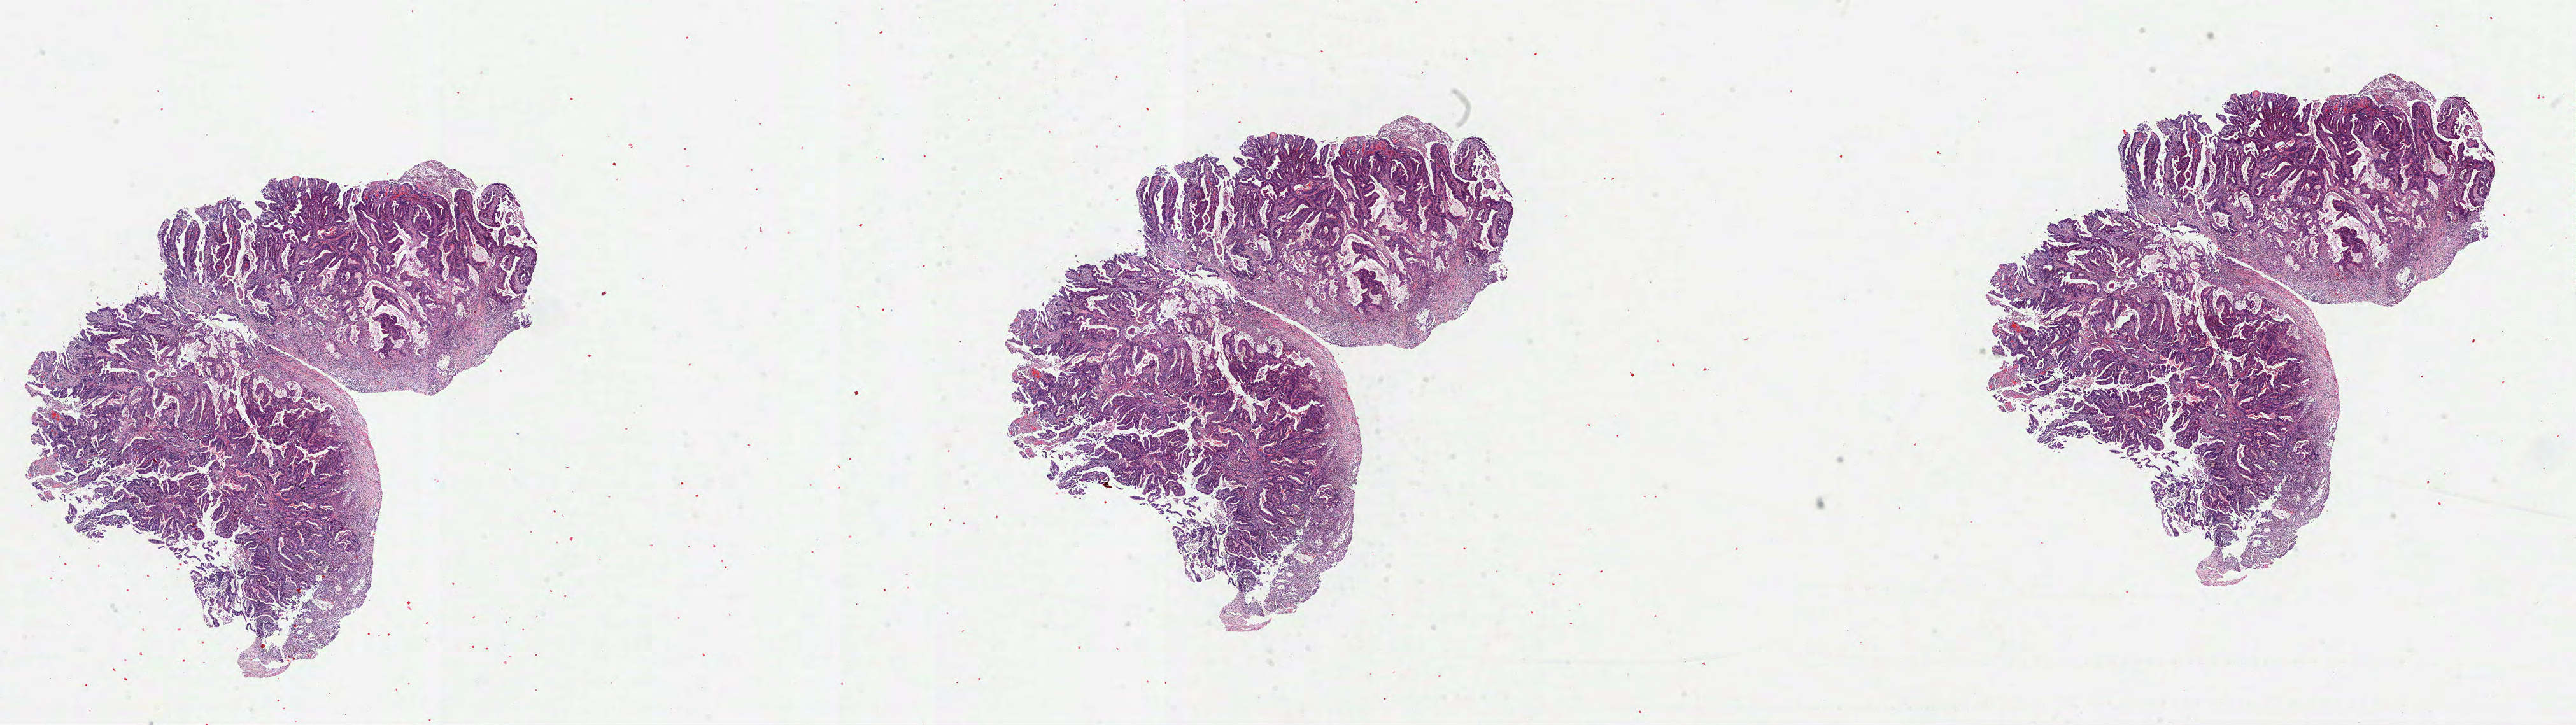
Digitized H&E-stained tissue section (whole slide) — a low-resolution overview of the entire scanned area, about 32.6 x 9.2 mm, frozen section, sample: primary tumour, colon. Female patient; age at initial diagnosis 69 years. Pathologist review of this section (percent, as recorded): tumour cells 80%, tumour nuclei 75%, normal cells 0%, stromal cells 20%, necrosis 0%.
• lymph nodes positive (case pathology): 0 of 16 examined
• AJCC pathologic stage: I (7th edition)
• diagnosis: Adenocarcinoma, NOS